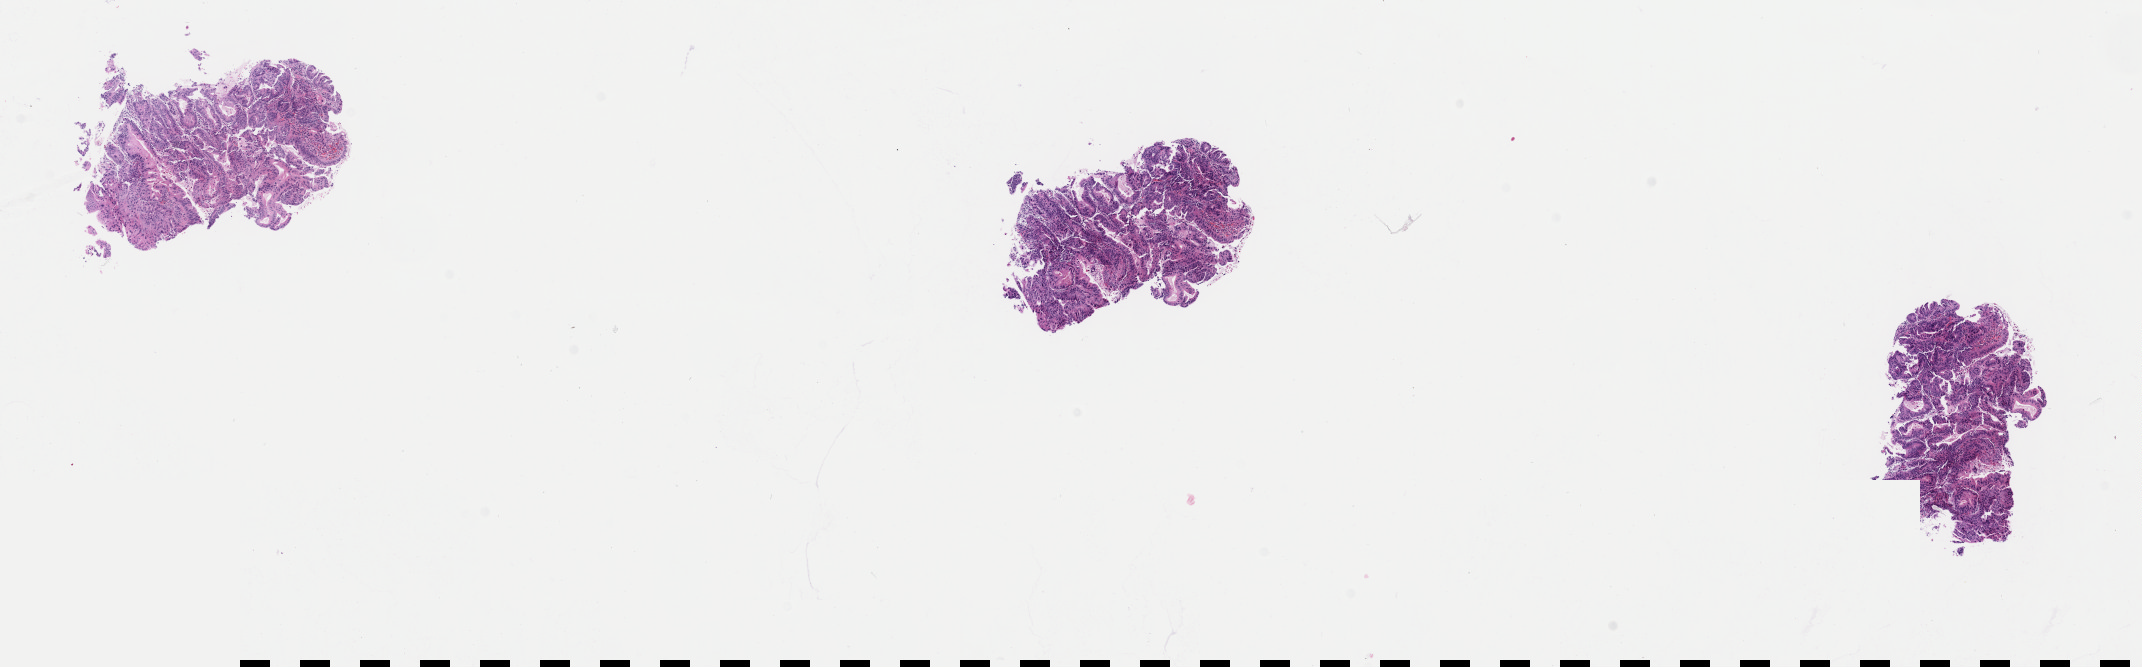
H&E-stained whole-slide image — a low-resolution overview of the entire scanned area, about 16.9 x 5.3 mm (slide scanned at 40x). Formalin-fixed paraffin-embedded (FFPE) diagnostic section. Primary tumour sample from the esophagus. Patient: male, age at initial diagnosis 64 years. Histologic grade: G2 (moderately differentiated). Slide review estimates, as recorded: tumour cells 70%, tumour nuclei 70%, normal cells 0%, stromal cells 30%, necrosis 0%. Infiltration values recorded for this section: lymphocyte infiltration 10%, monocyte infiltration 0%, neutrophil infiltration 0%.
Pathologic diagnosis: Adenocarcinoma, NOS (lower third of esophagus).